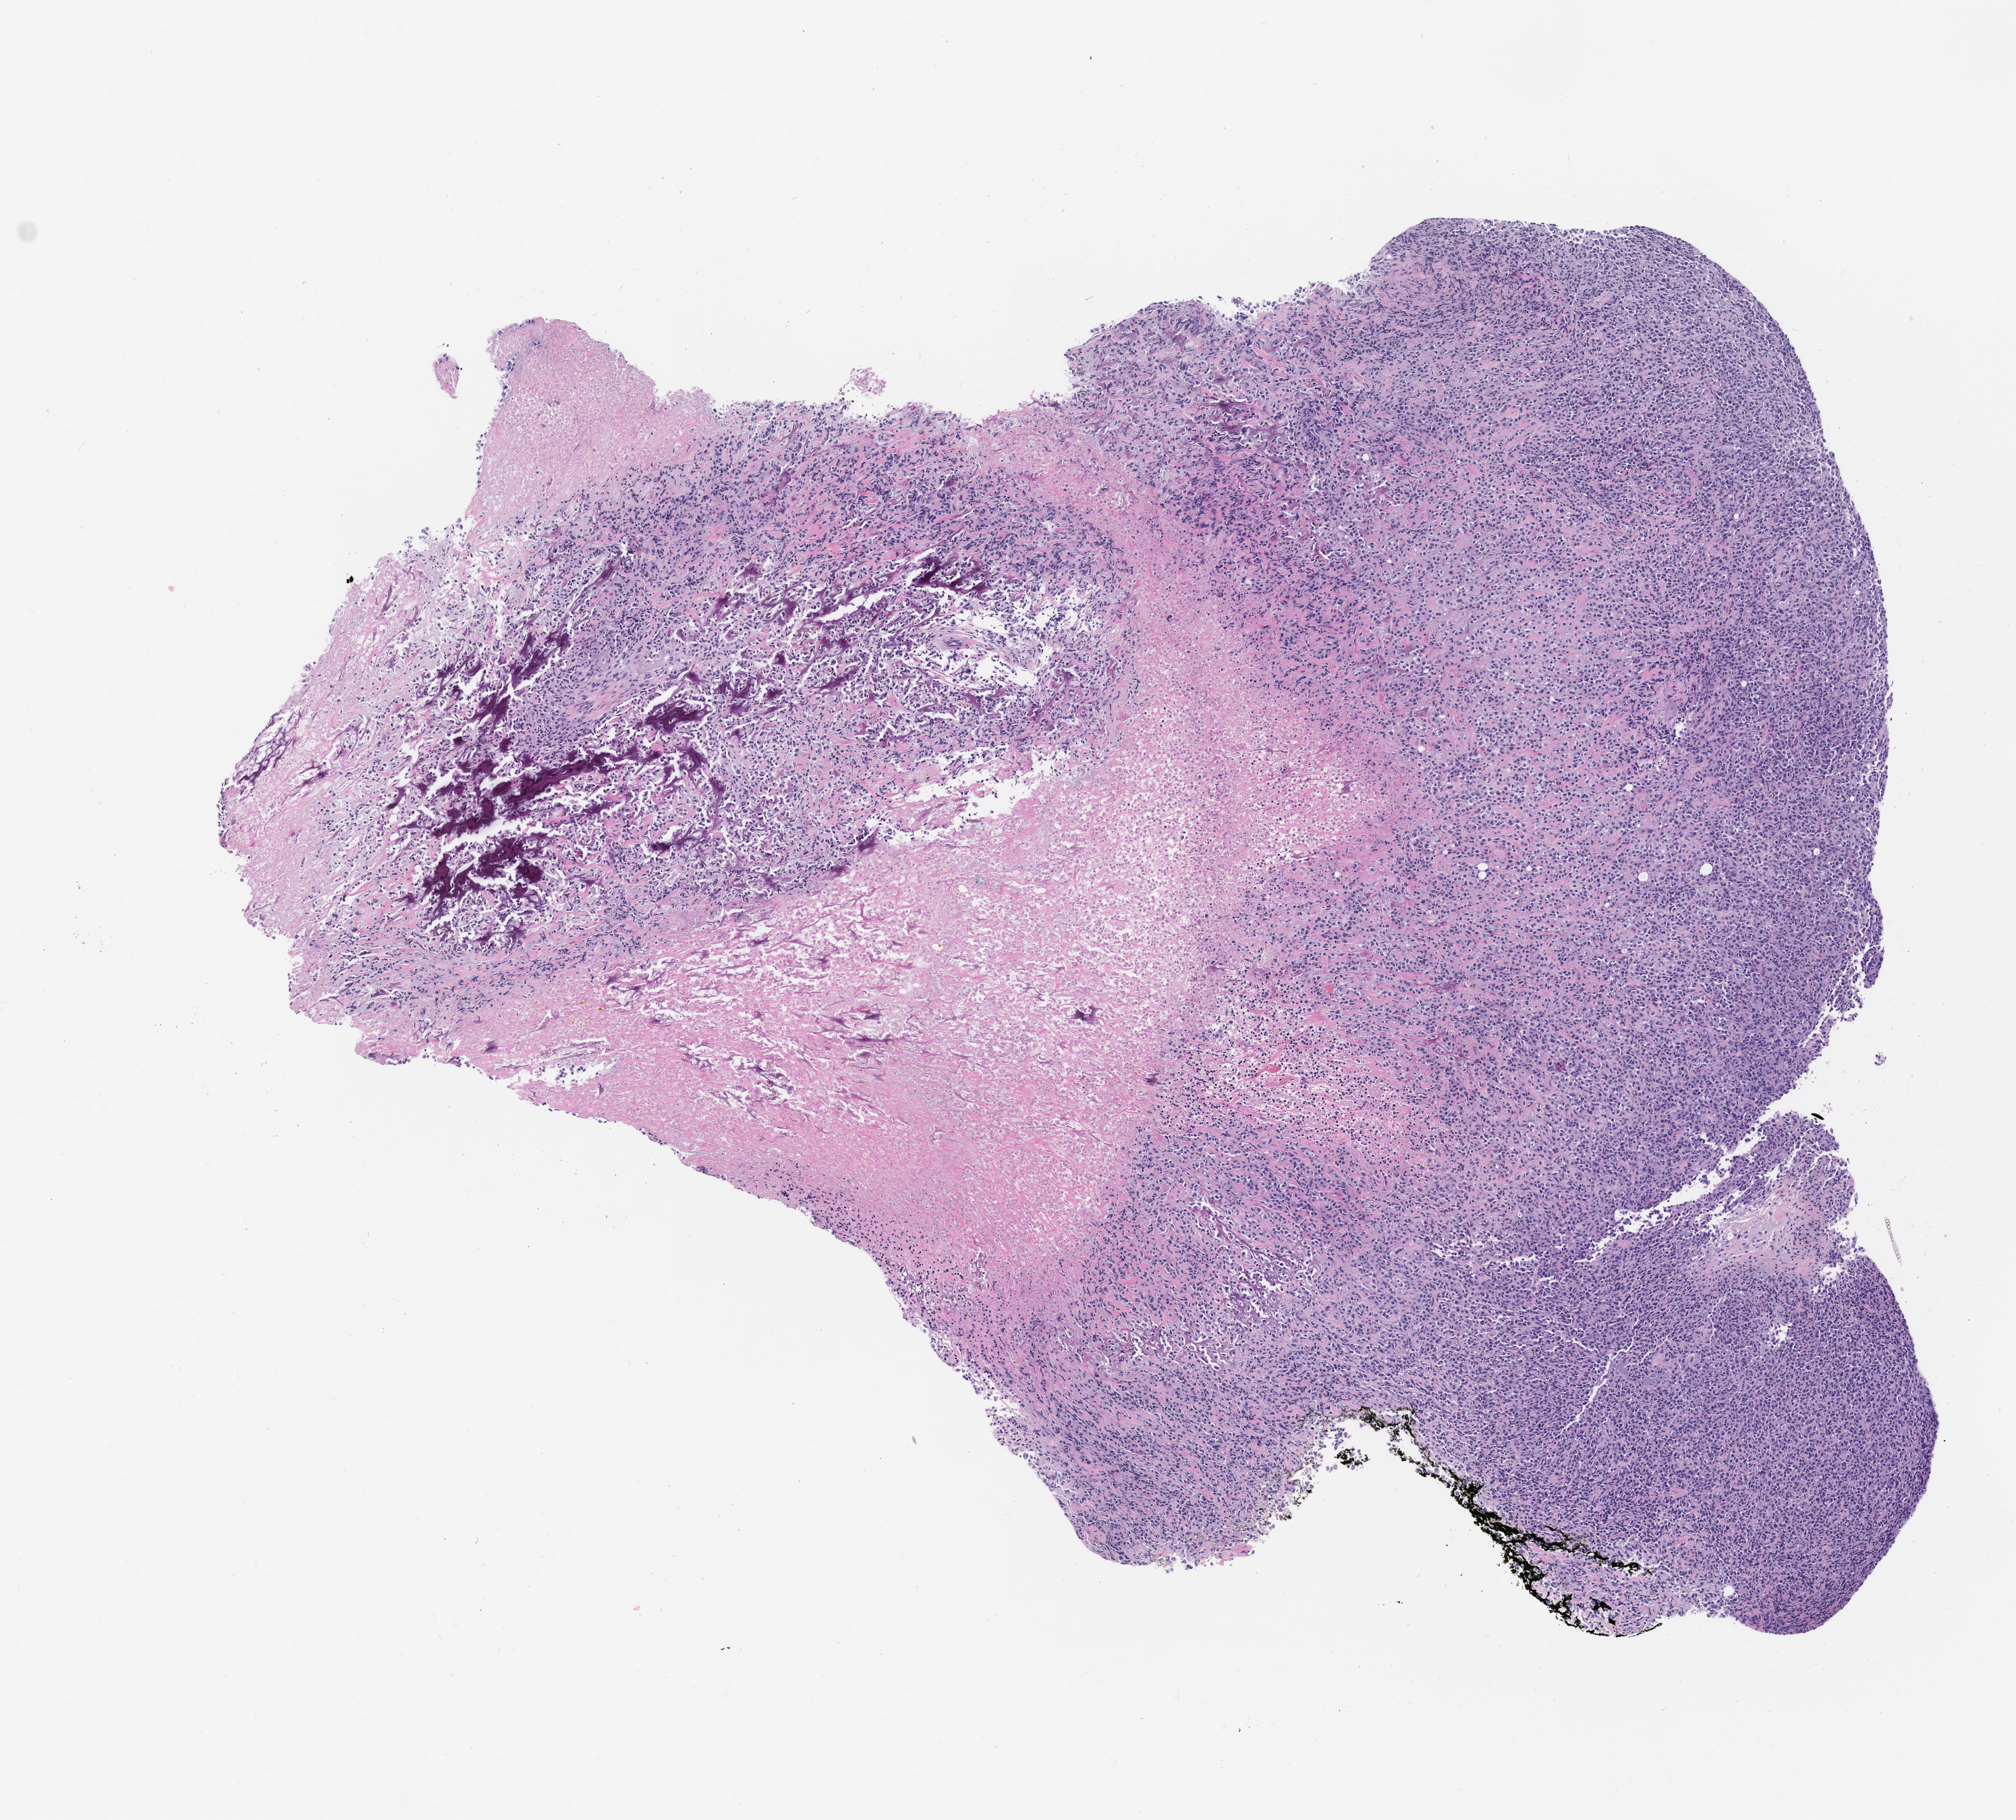
Whole-slide image, H&E: patient-derived xenograft (human tumor grown in a mouse), passage 2, a low-resolution overview of the entire scanned area, about 6.0 x 5.4 mm, formalin-fixed paraffin-embedded section, originating tumor site category: bone.
Originating patient diagnosis: Osteosarcoma.